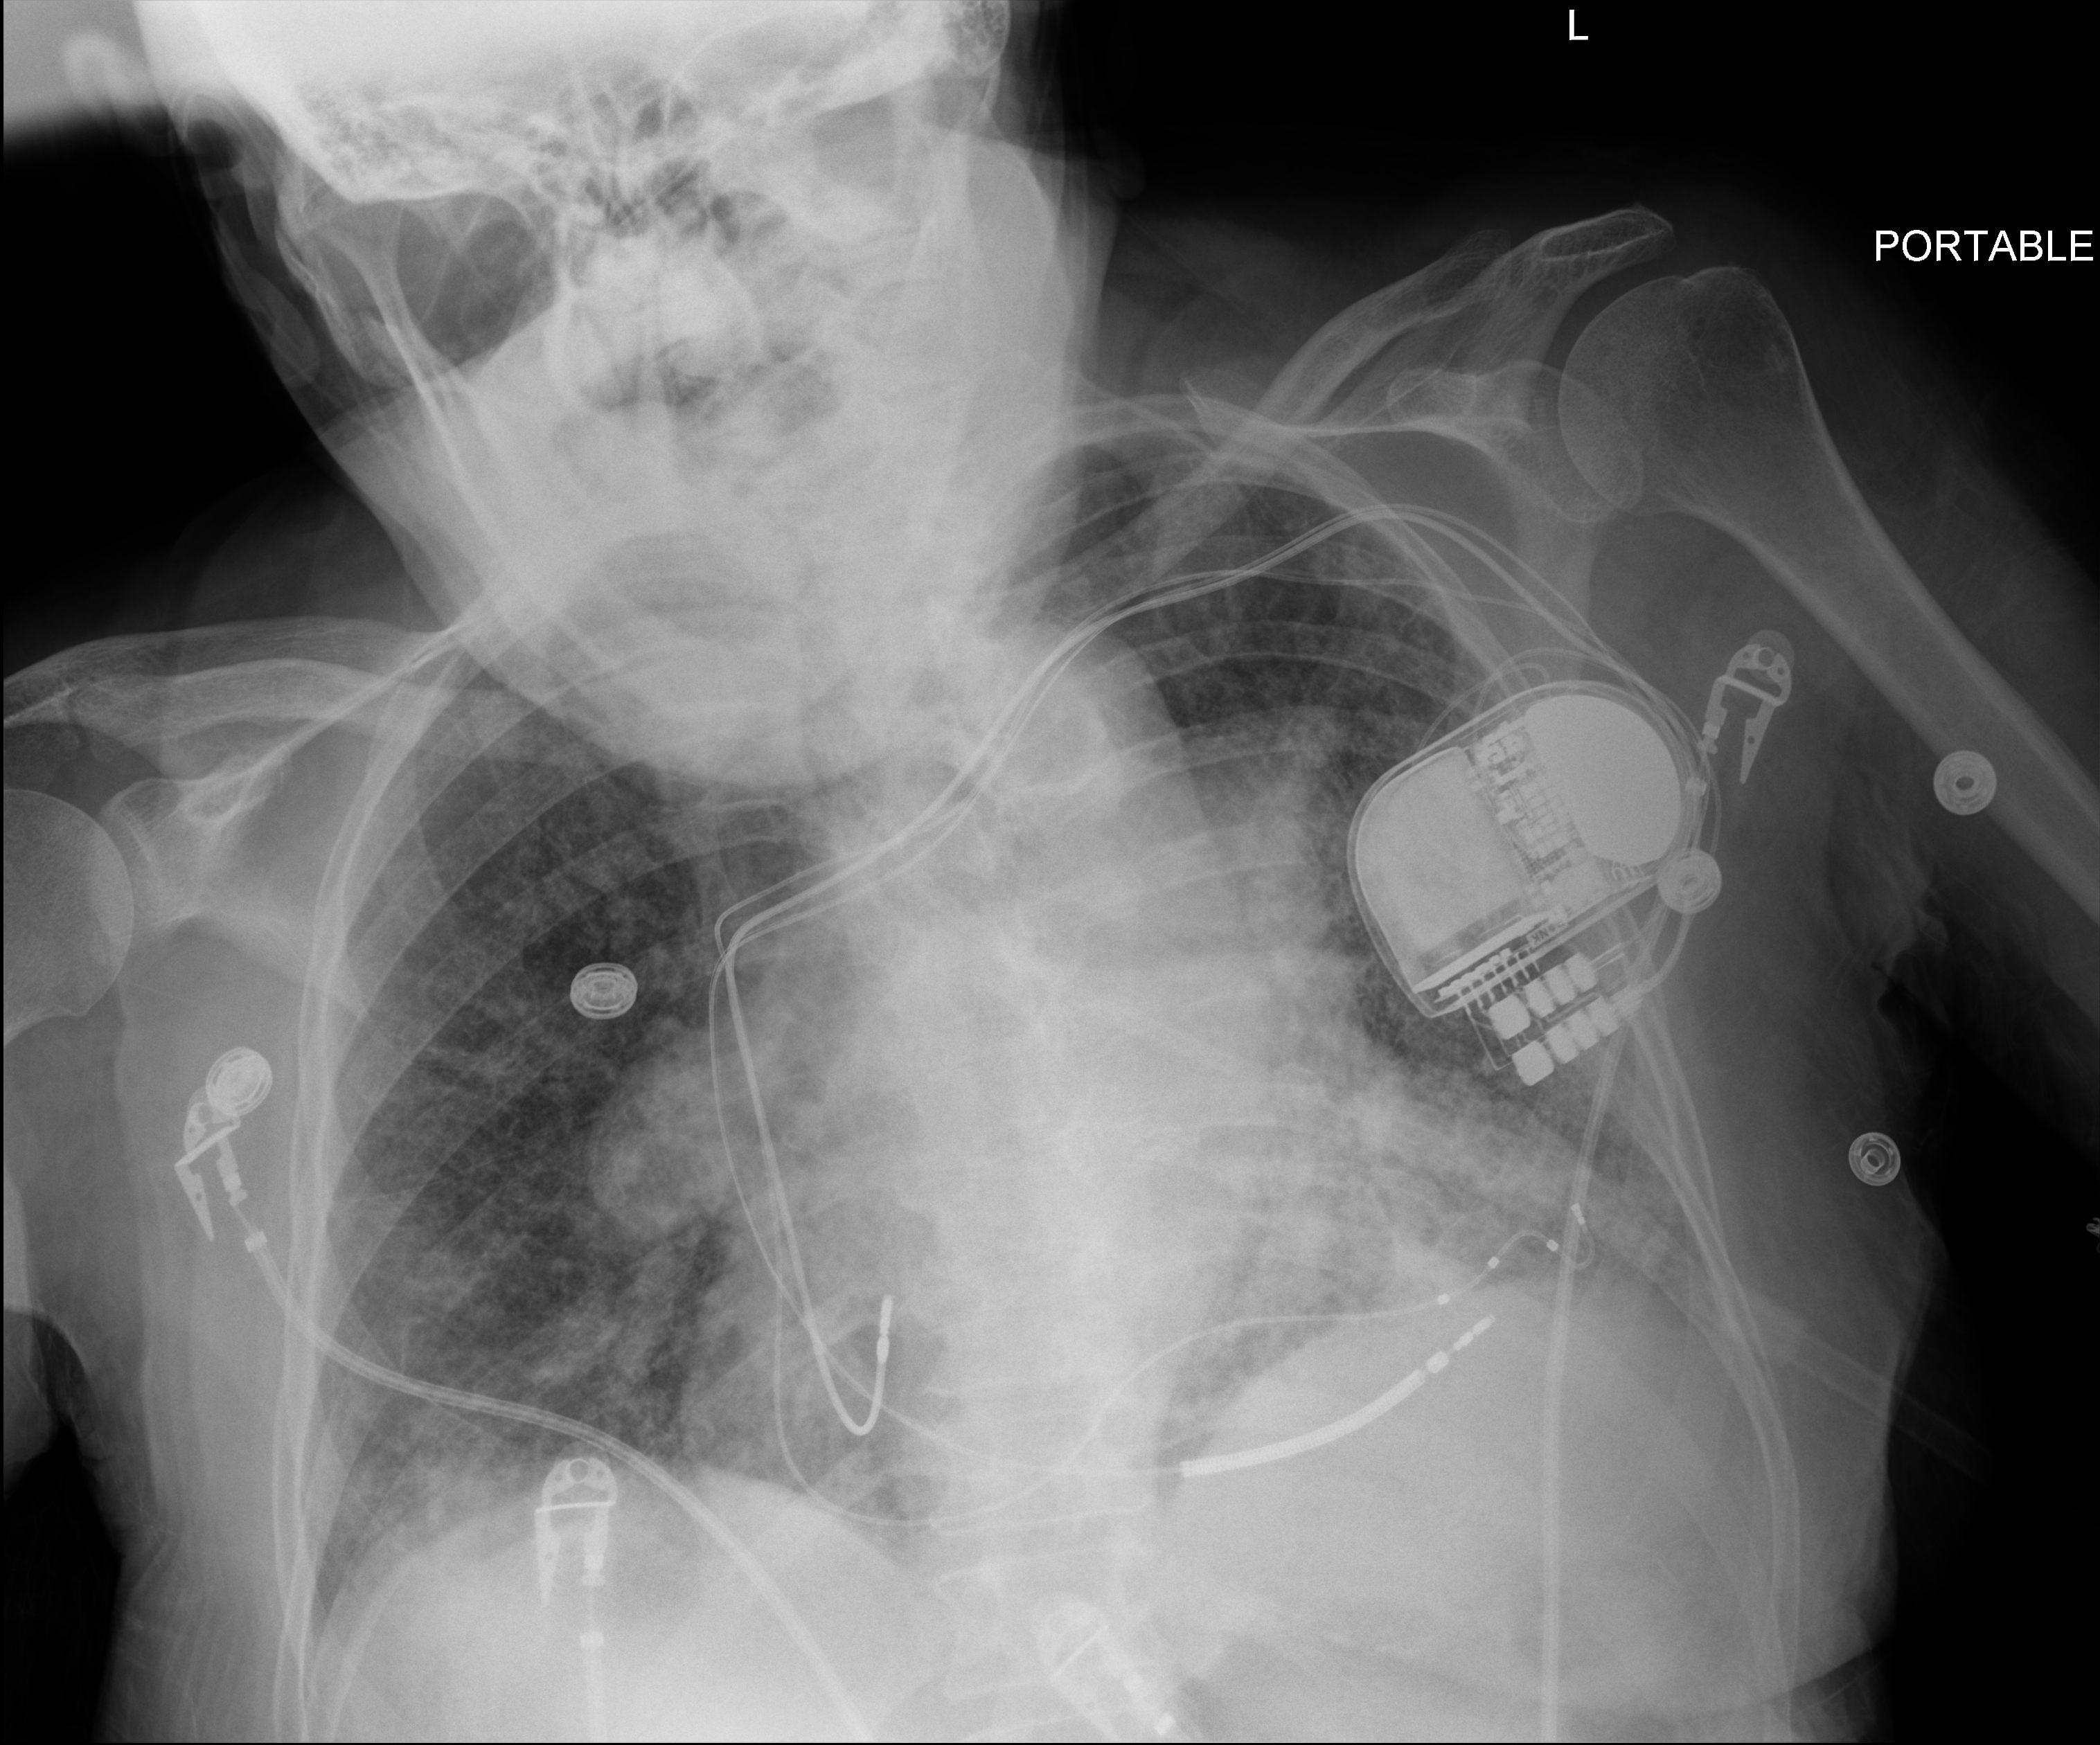
Chest X-ray (portable), anteroposterior (AP) projection. Female patient hospitalised with COVID-19, age 60–74 years.
Hospital-stay facts (about this admission, not read from this image; timing relative to this image not recorded):
- length of hospital stay: 6 days
- mechanically ventilated during this hospital stay: no